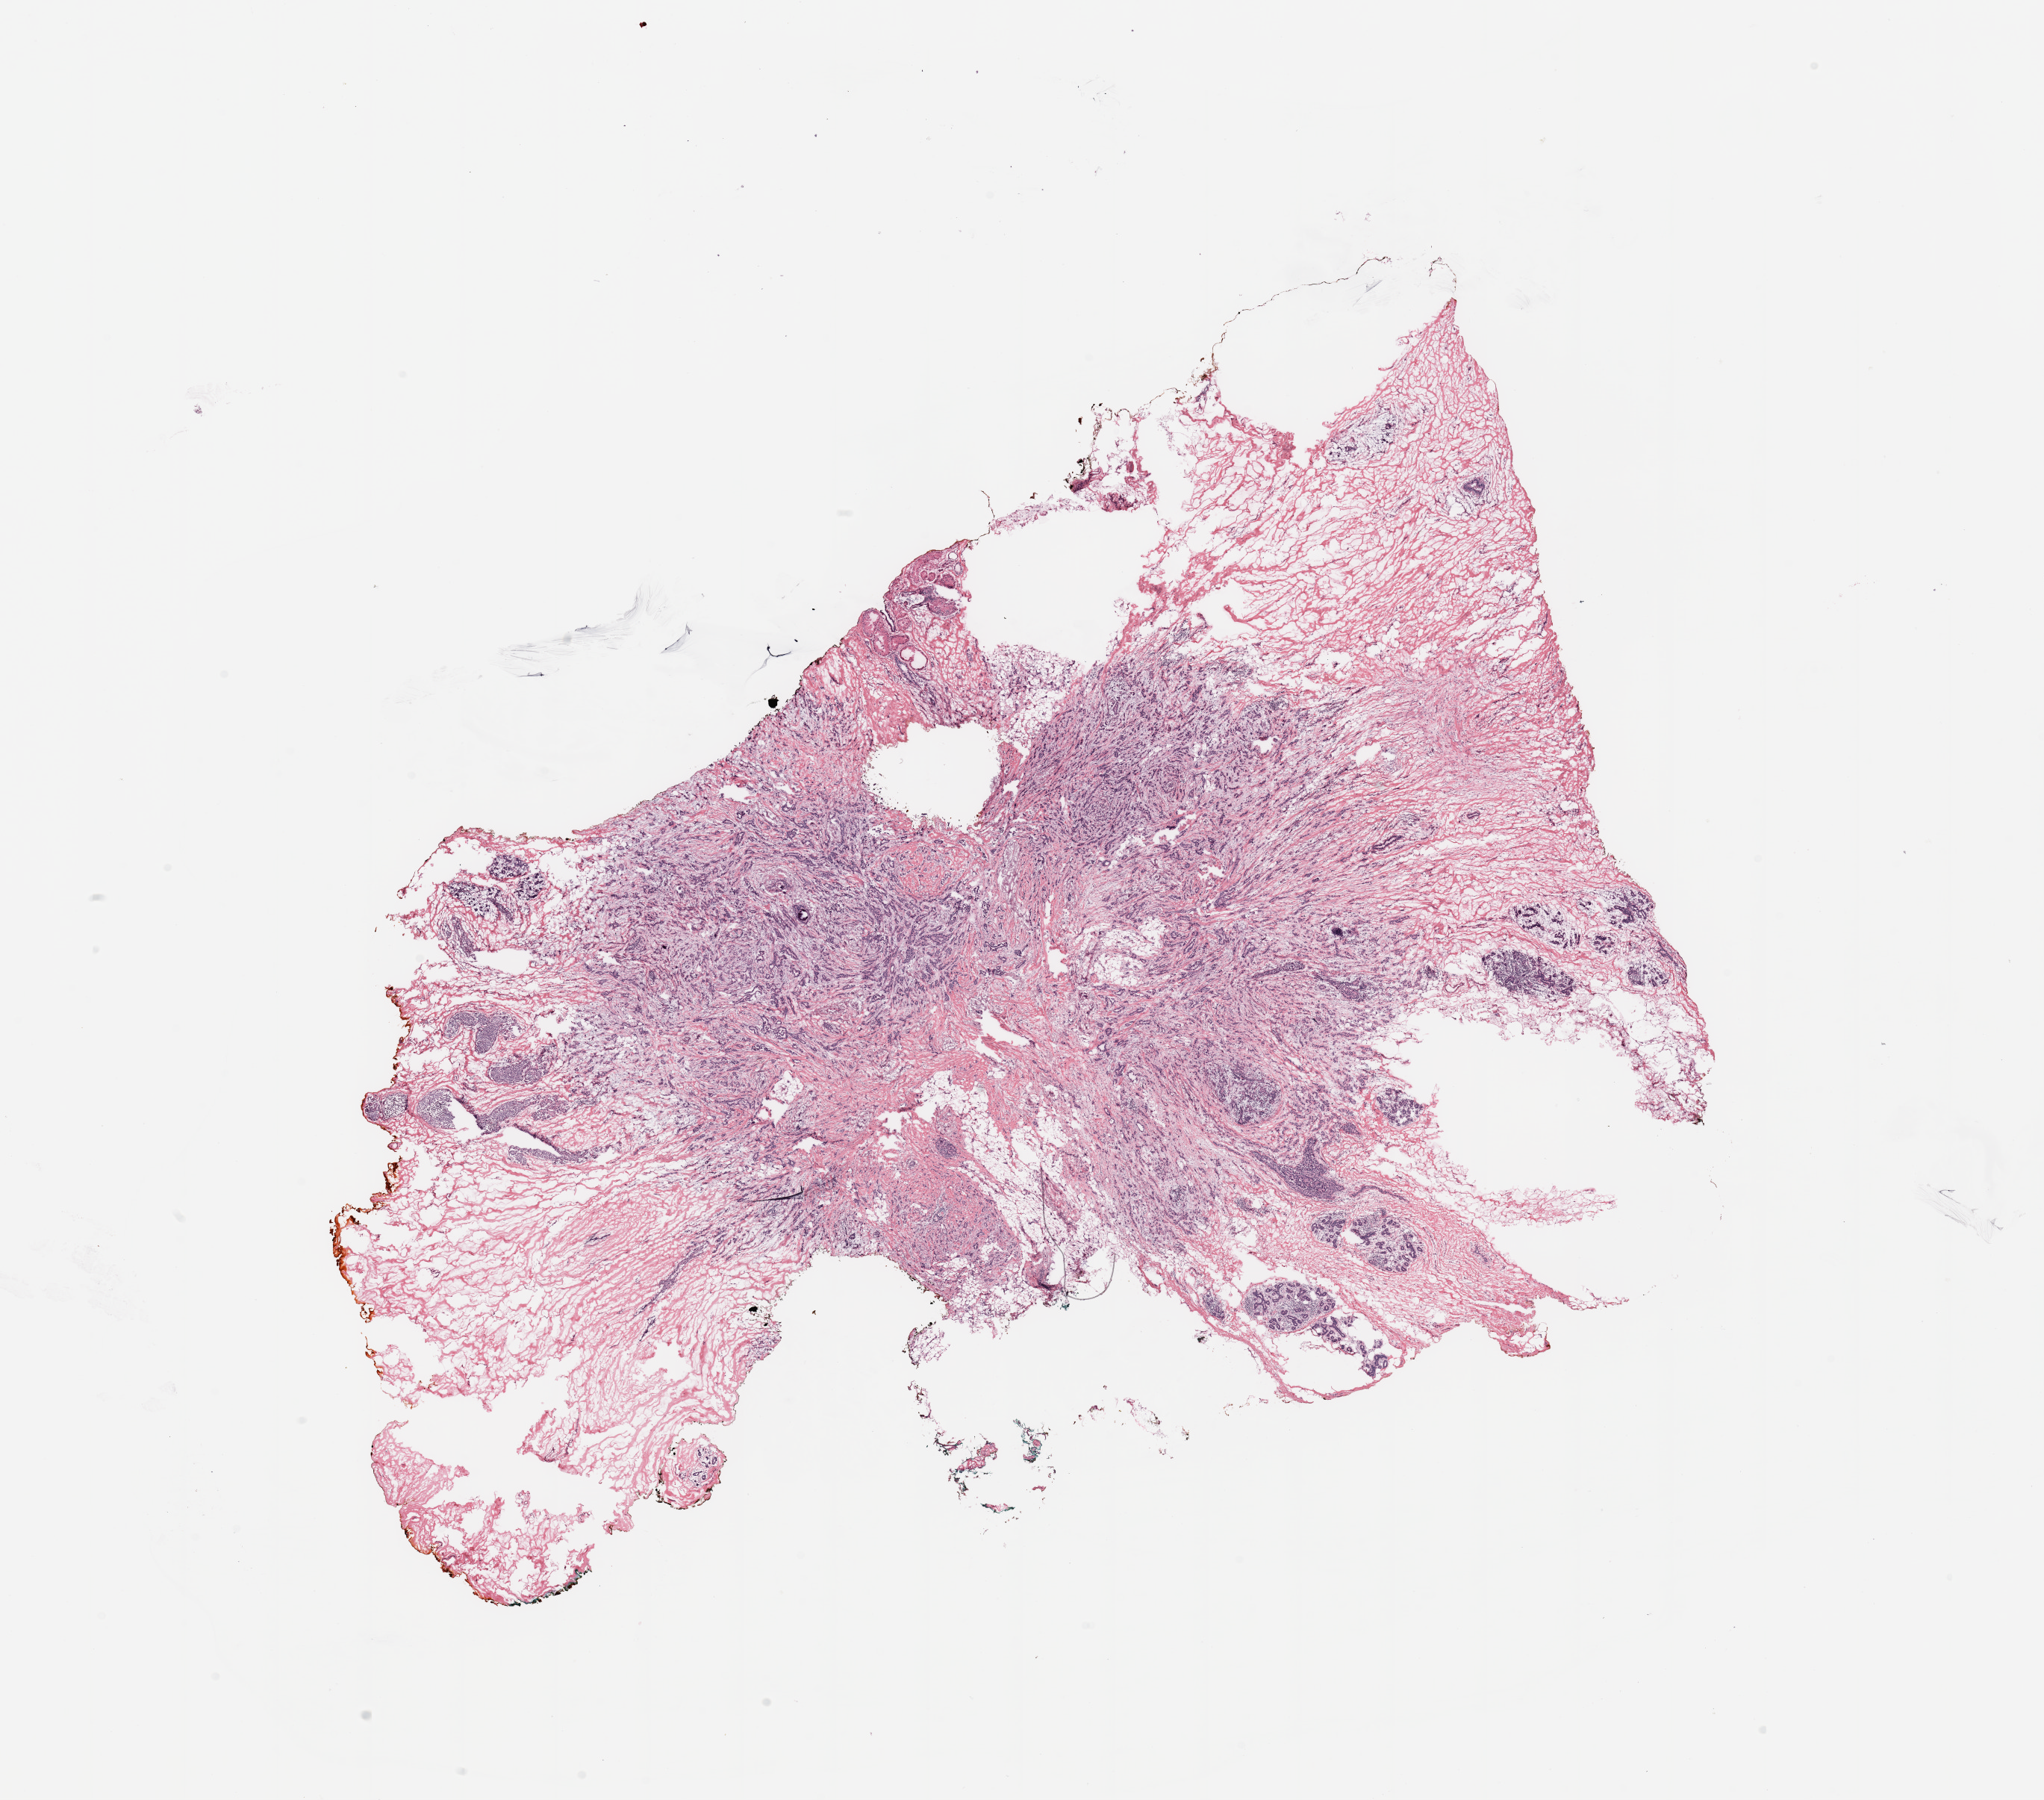
Whole-slide histology image, H&E — low-resolution overview of the scanned area, about 21.7 x 19.1 mm (slide scanned at 20x), breast, tissue type not recorded.
• patient diagnosis (cohort enrolment): breast cancer (breast)